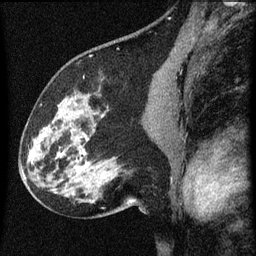
Breast MRI (dynamic contrast-enhanced), one sagittal slice; slice 36 of 60 in the series (ordered by position); dynamic contrast-enhanced series, image 2 of 3 at this slice position (ordered by acquisition); 1.5 T; TE 4.2 ms, TR 8 ms; 256 × 256 image matrix, field of view 180 × 180 mm. Female patient, age 61 years.
Annotated regions visible in this slice (semi-automatically segmented with operator editing):
- analysis volume of interest (the breast-tissue region the enhancement analysis was run in; not a lesion): bounding box <27,80,139,209> (left, top, right, bottom; pixels)
- tumour enhancement mask (voxels above the 70 % enhancement threshold inside the analysis volume of interest): <42,134,44,137>